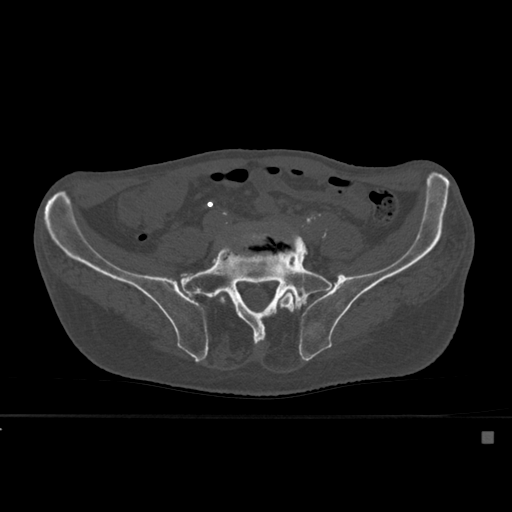
CT including the spine, one axial slice. Position 164 of 527 along the scan axis. Bone window (W 1800 / L 400 HU). 512 × 512 image matrix. Male patient, age 78 years. Case-level facts recorded for this patient, not image findings: primary cancer: prostate.
Outlined on this slice (semi-automatically segmented with operator editing):
- L5 vertebra: bounding box <219,231,294,313> (left, top, right, bottom; pixels)